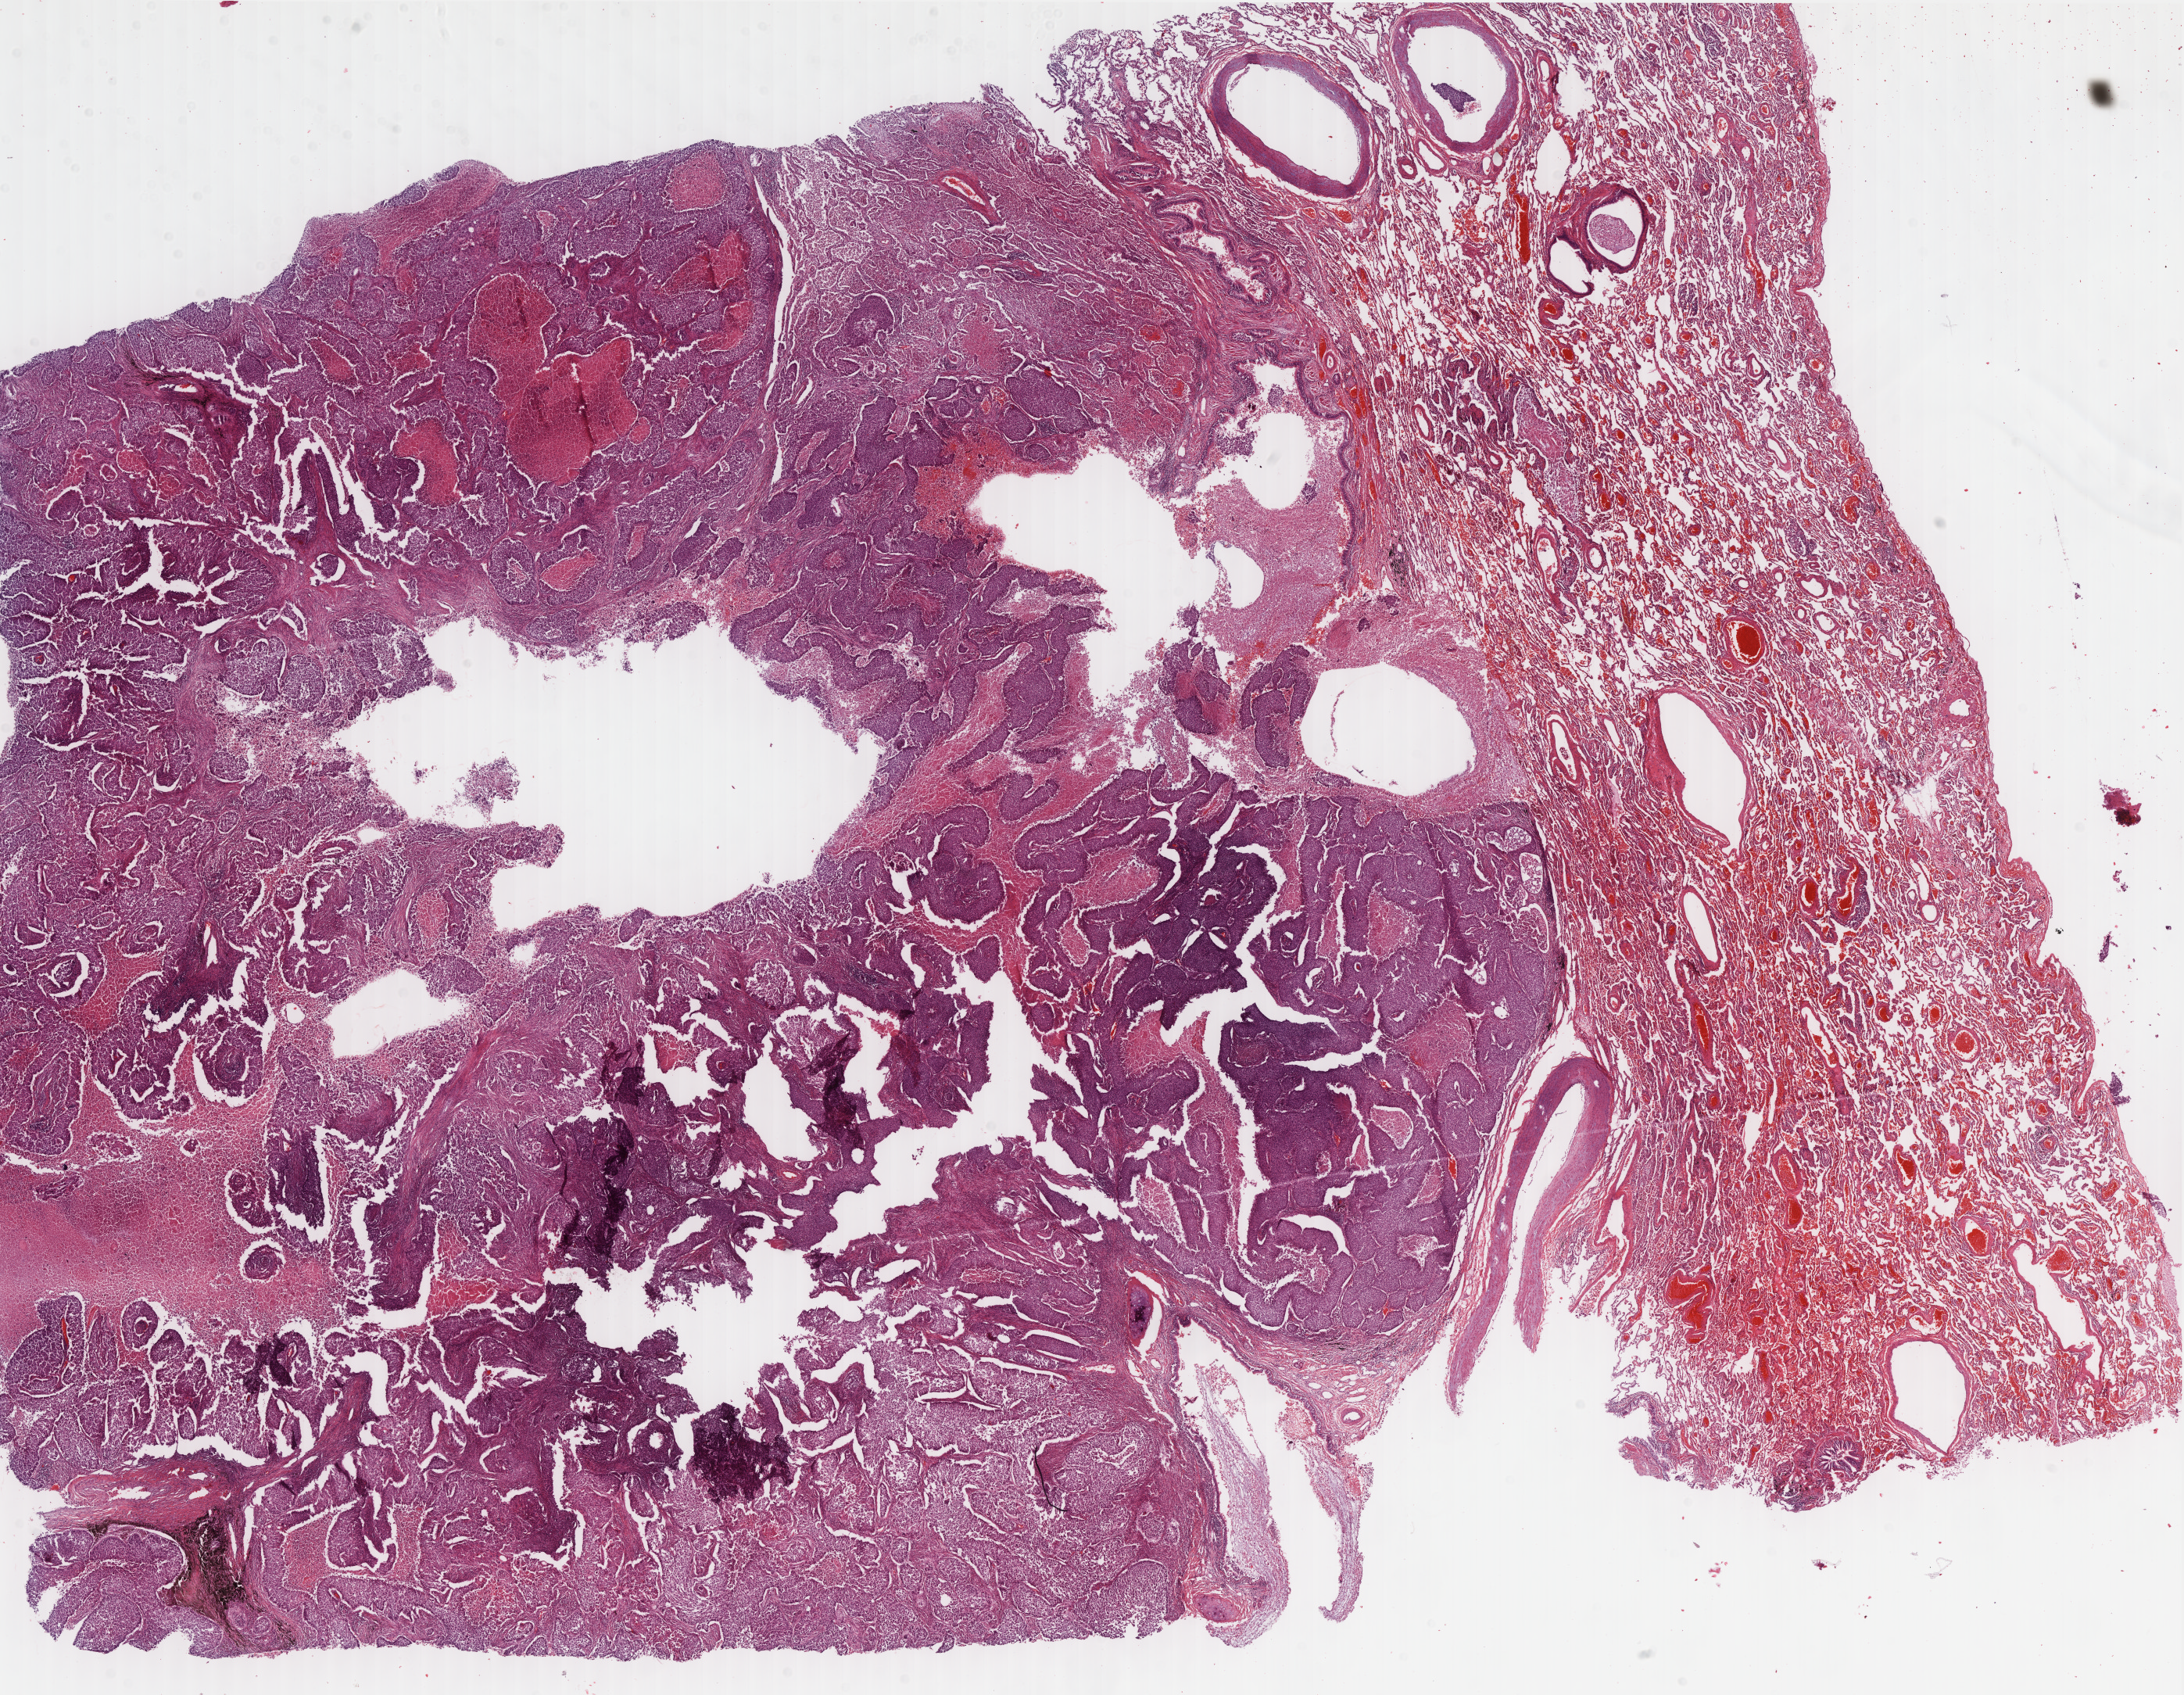
H&E-stained whole-slide image, shown as a low-resolution overview of the whole scanned area (about 22.5 x 17.5 mm, acquisition: 40x scan), FFPE section, primary tumour sample from the lung. Patient: male, age at initial diagnosis 73 years.
Diagnosis: Basaloid squamous cell carcinoma (upper lobe, lung). AJCC pathologic stage: IIIA (6th edition). TNM: T2 N2 M0.